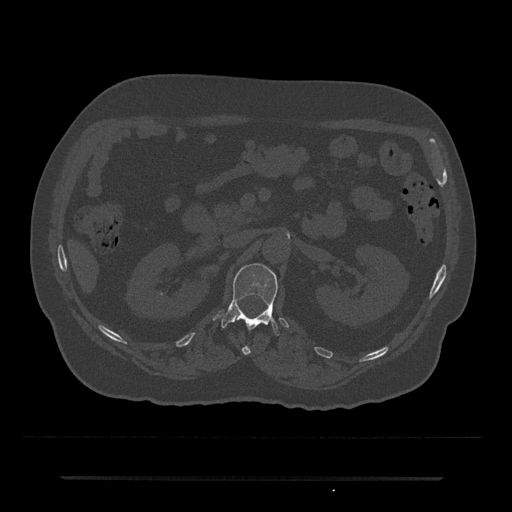
CT including the spine, one axial slice. Position 76 of 797 along the scan axis. Reconstruction kernel Br40s/3. Bone window (W 1800 / L 400 HU). 0.5 mm slice thickness. 512 × 512 image matrix, field of view 437 × 437 mm. Male patient, age 69 years. From the clinical record (not read from this slice): primary cancer: prostate.
Annotated regions visible in this slice (semi-automatically segmented with operator editing):
- L1 vertebra: bounding box (x1, y1, x2, y2) in pixels: (221, 263, 280, 336)
- T12 vertebra: (242, 346, 251, 355)